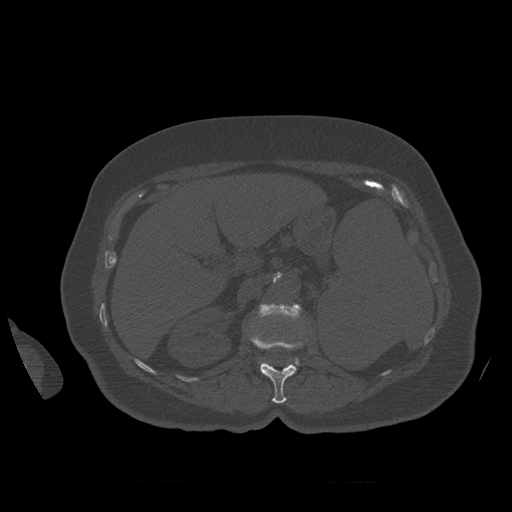
CT including the spine, one axial slice. Position 270 of 399 along the scan axis. Reconstruction kernel STANDARD. 120 kVp. Bone window (W 1800 / L 400 HU). 512 × 512 image matrix, field of view 404 × 404 mm. Patient age 81 years. From the clinical record (not read from this slice): primary cancer: renal; vertebrae with lytic lesions (as recorded): L1.
Annotated regions visible in this slice (semi-automatically segmented with operator editing):
- L1 vertebra: bounding box <251,335,301,404> (left, top, right, bottom; pixels)
- L2 vertebra: <259,304,302,366>